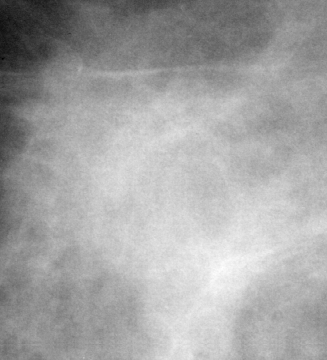
Cropped region of a digitized screen-film mammogram centred on a radiologist-marked abnormality, right breast, CC view, BI-RADS breast density category 3 (scale 1–4).
- Marked abnormality: mass, shape irregular, margins ill defined; BI-RADS assessment category 4; subtlety rating 4 on a 1 (subtle) to 5 (obvious) scale; pathology (as recorded): malignant.